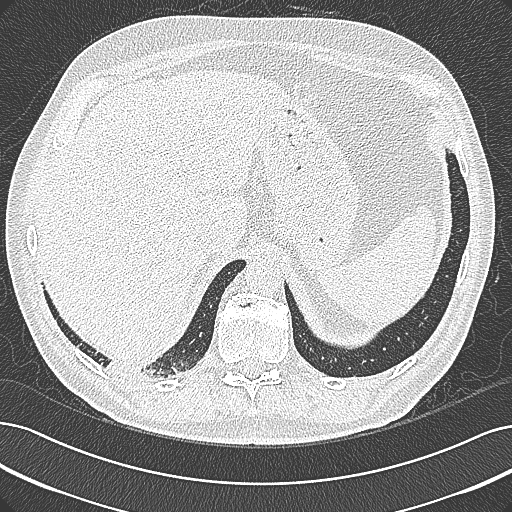
Low-dose screening chest CT, axial slice, baseline screening round, lung window (W 1500 / L -600 HU), slice 265 of 355 in the series. Male, age 68 years at enrolment. Former smoker at enrolment.
Expert reader's lesion annotation, box from (x=93, y=335) to (x=198, y=395) px. Screening reader's record for this exam: no non-calcified nodule ≥4 mm recorded. Official screen result: negative screen, significant abnormalities not suspicious for lung cancer. Lung cancer was diagnosed 154 days after this screen: mucinous adenocarcinoma, right lower lobe, well differentiated (G1), stage IB (AJCC 6th edition), 50 mm at pathology.